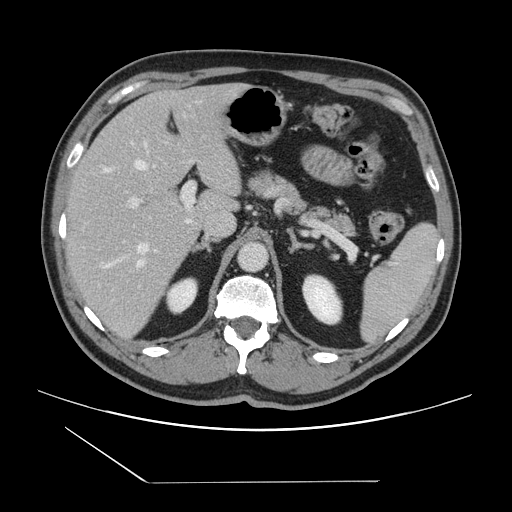
Contrast-enhanced abdominal CT, one axial slice. Slice 91 of 157 in the series (ordered by position). Intravenous contrast given. Soft-tissue window (W 400 / L 40 HU). 2.5 mm slice thickness. 512 × 512 image matrix, field of view 407 × 407 mm. Male patient, age 61 years. Case-level facts recorded for this patient, not image findings: diagnosis: colorectal cancer liver metastases, imaged before liver resection; multiple liver metastases: yes; largest metastasis: 5.5 cm.
Structures marked on this image (outlined manually by an expert reader):
- hepatic veins: bounding box (x1, y1, x2, y2) in pixels: (101, 143, 149, 268)
- liver: (63, 85, 243, 337)
- planned liver remnant (the part of the liver to remain after resection): (67, 84, 236, 222)
- portal vein (with intrahepatic branches): (128, 182, 195, 222)